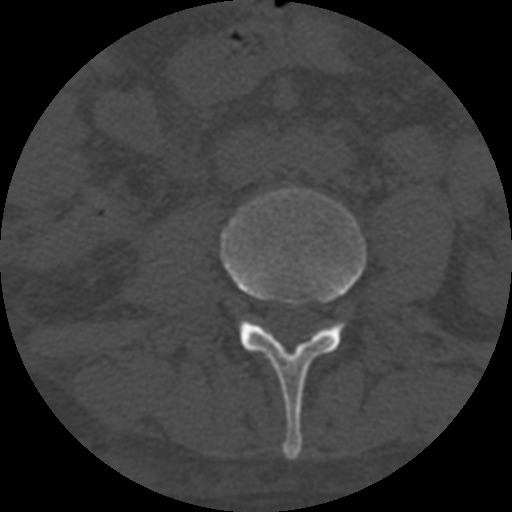
CT including the spine, one axial slice. Slice 229 of 708 in the series (ordered by position). Reconstruction kernel STANDARD. 120 kVp. One of 3 acquisitions stored at this slice position. Bone window (W 1800 / L 400 HU). 1.25 mm slice thickness. 512 × 512 image matrix. Patient age 55 years. From the clinical record (not read from this slice): primary cancer: colon; vertebrae with lytic lesions (as recorded): T12, L1, L5.
Outlined on this slice (semi-automatic segmentation, software-assisted and operator-edited):
- L3 vertebra: bounding box (x1, y1, x2, y2) in pixels: (221, 186, 366, 460)